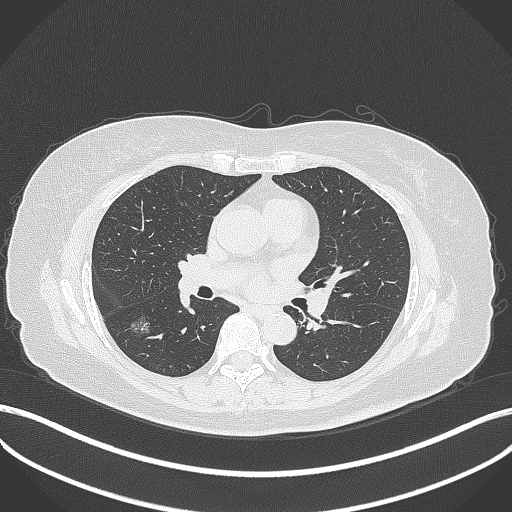
Chest CT, one axial slice; slice 170 of 322 in the series (ordered by position); reconstruction kernel B70f; 120 kVp; lung window (W 1500 / L -600 HU); 1 mm slice thickness; 512 × 512 image matrix, field of view 400 × 400 mm. Patient: female, 64 years. From the clinical record (not read from this slice): clinical TNM (as recorded): T1c N0 M0; histopathological grade: G1.
Annotated regions visible in this slice (rectangle marked by the reading radiologist):
- lung tumour (recorded histology: adenocarcinoma): bounding box (x1, y1, x2, y2) in pixels: (124, 307, 151, 337)